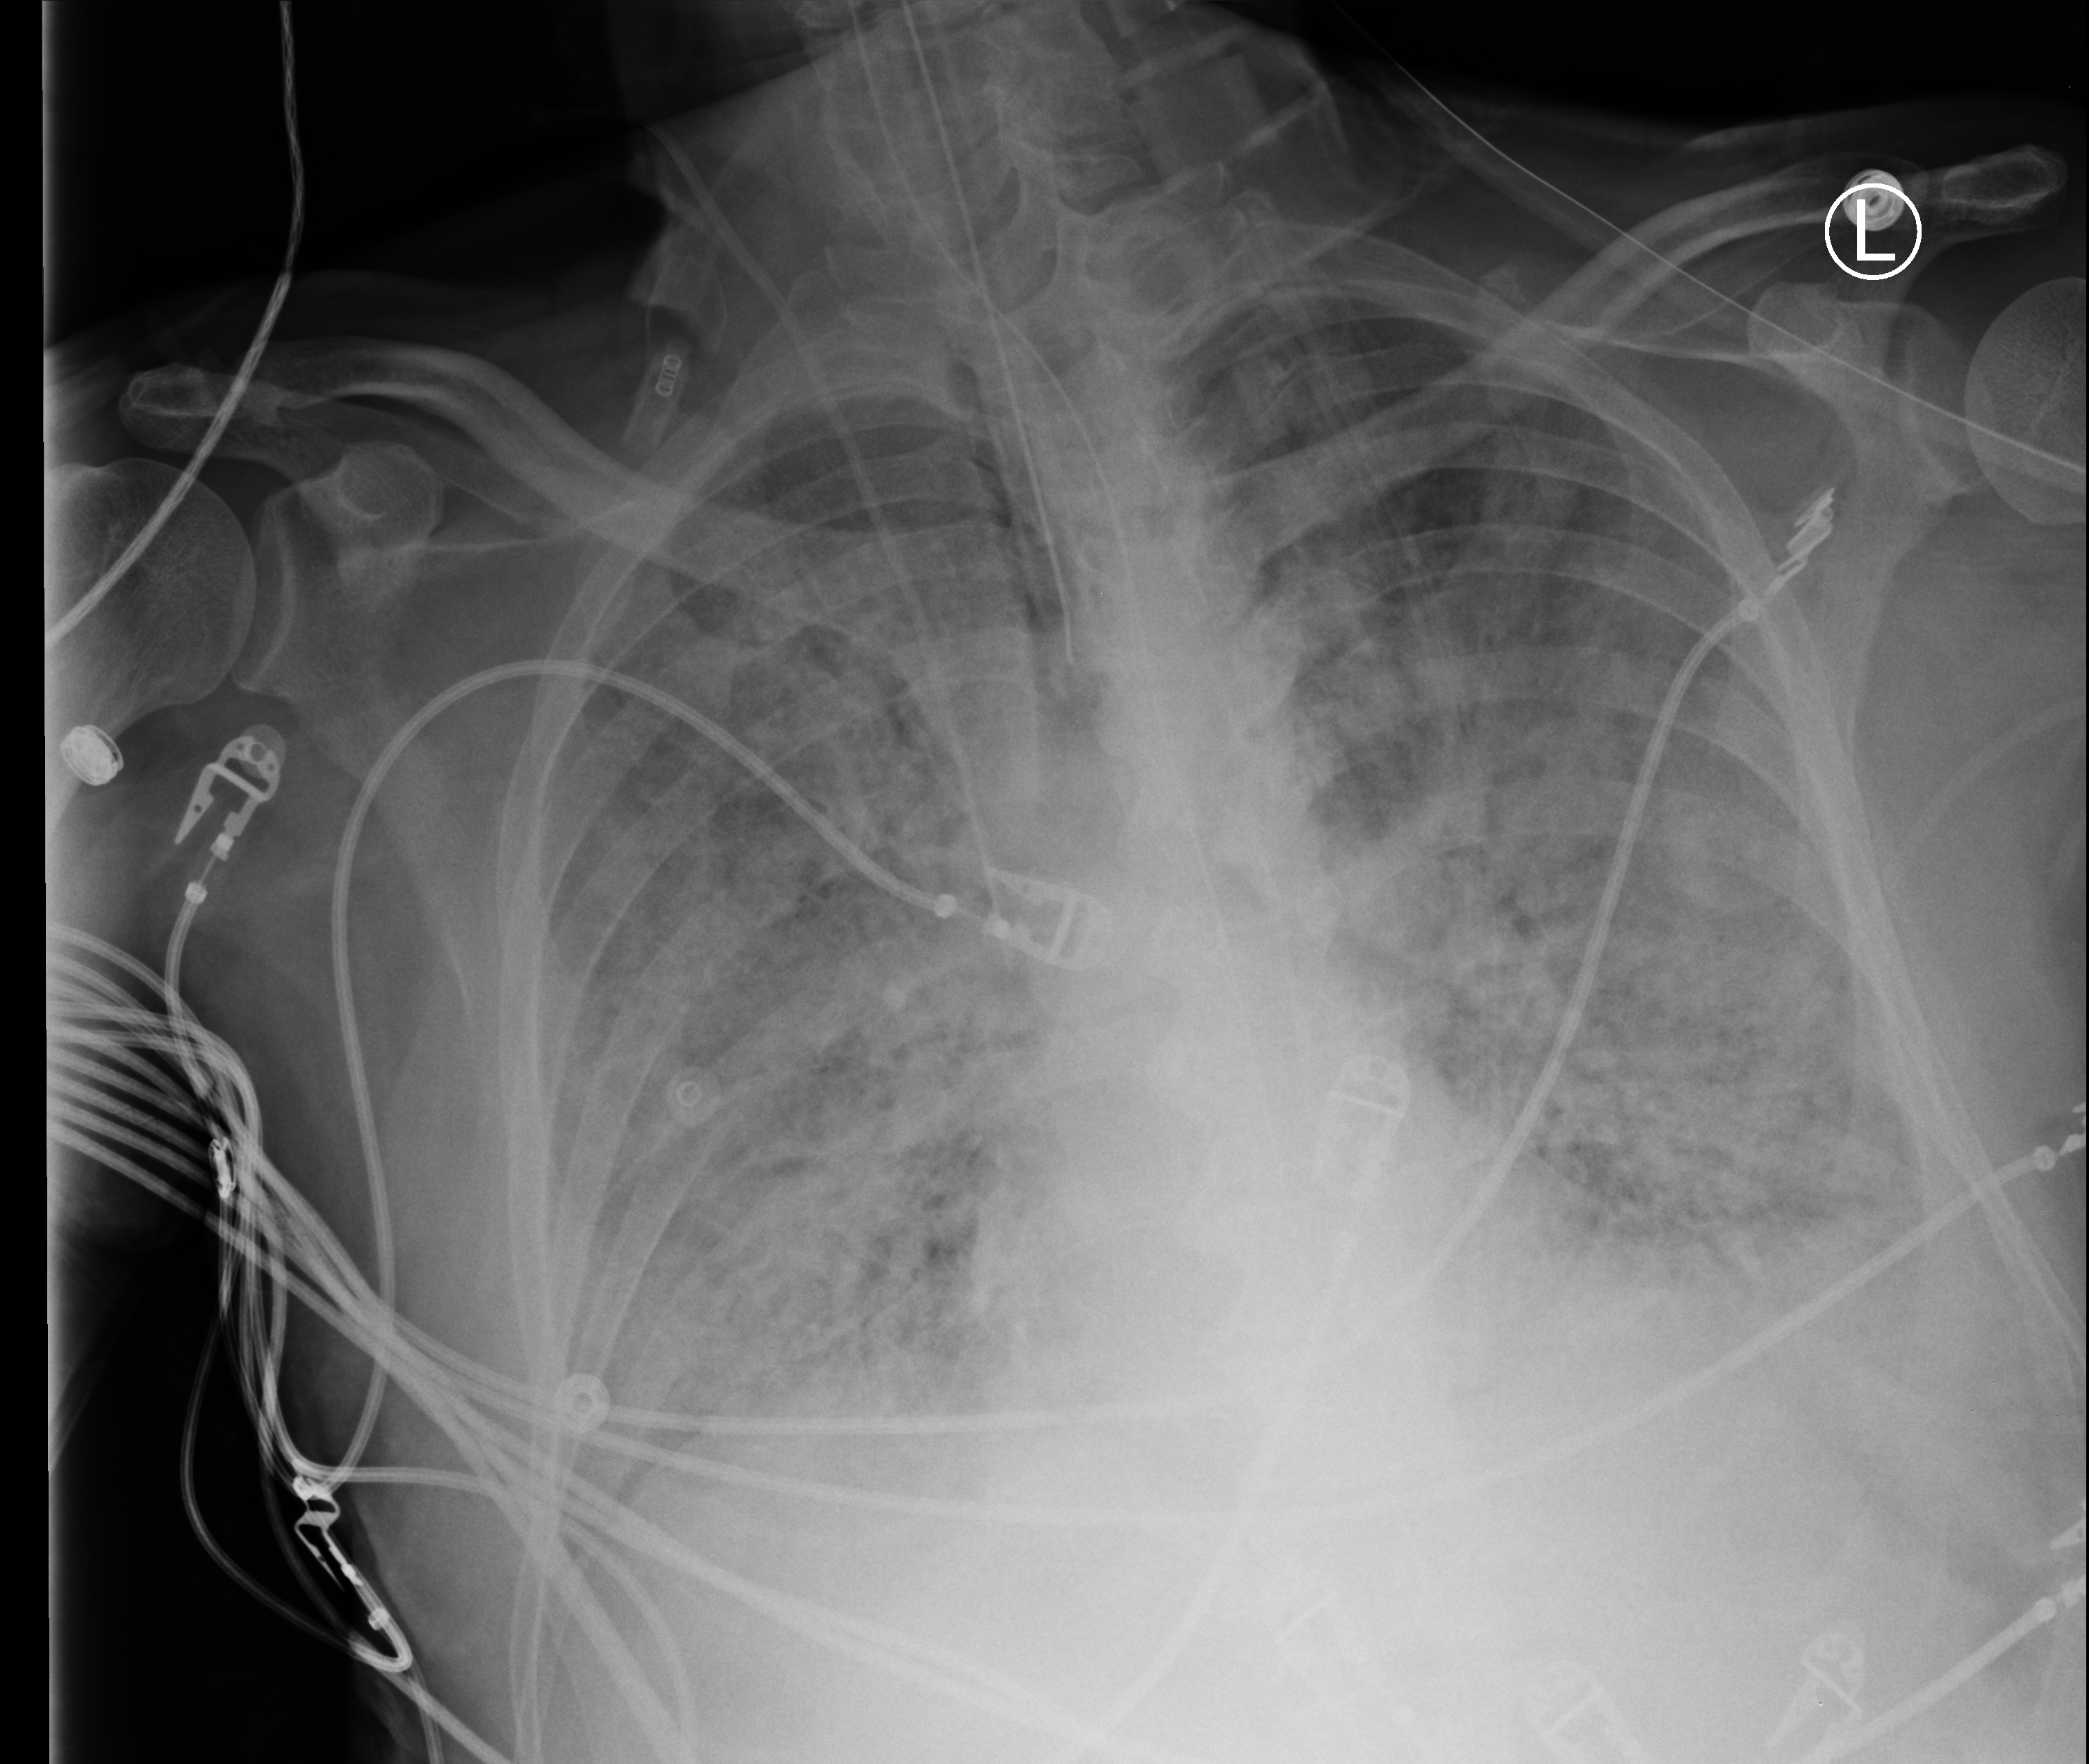
Chest X-ray (portable); anteroposterior (AP) projection. Male patient hospitalised with COVID-19, age 60–74 years.
Hospital-stay facts (about this admission, not read from this image; timing relative to this image not recorded): length of hospital stay: 15 days; diabetes (admission record): yes.